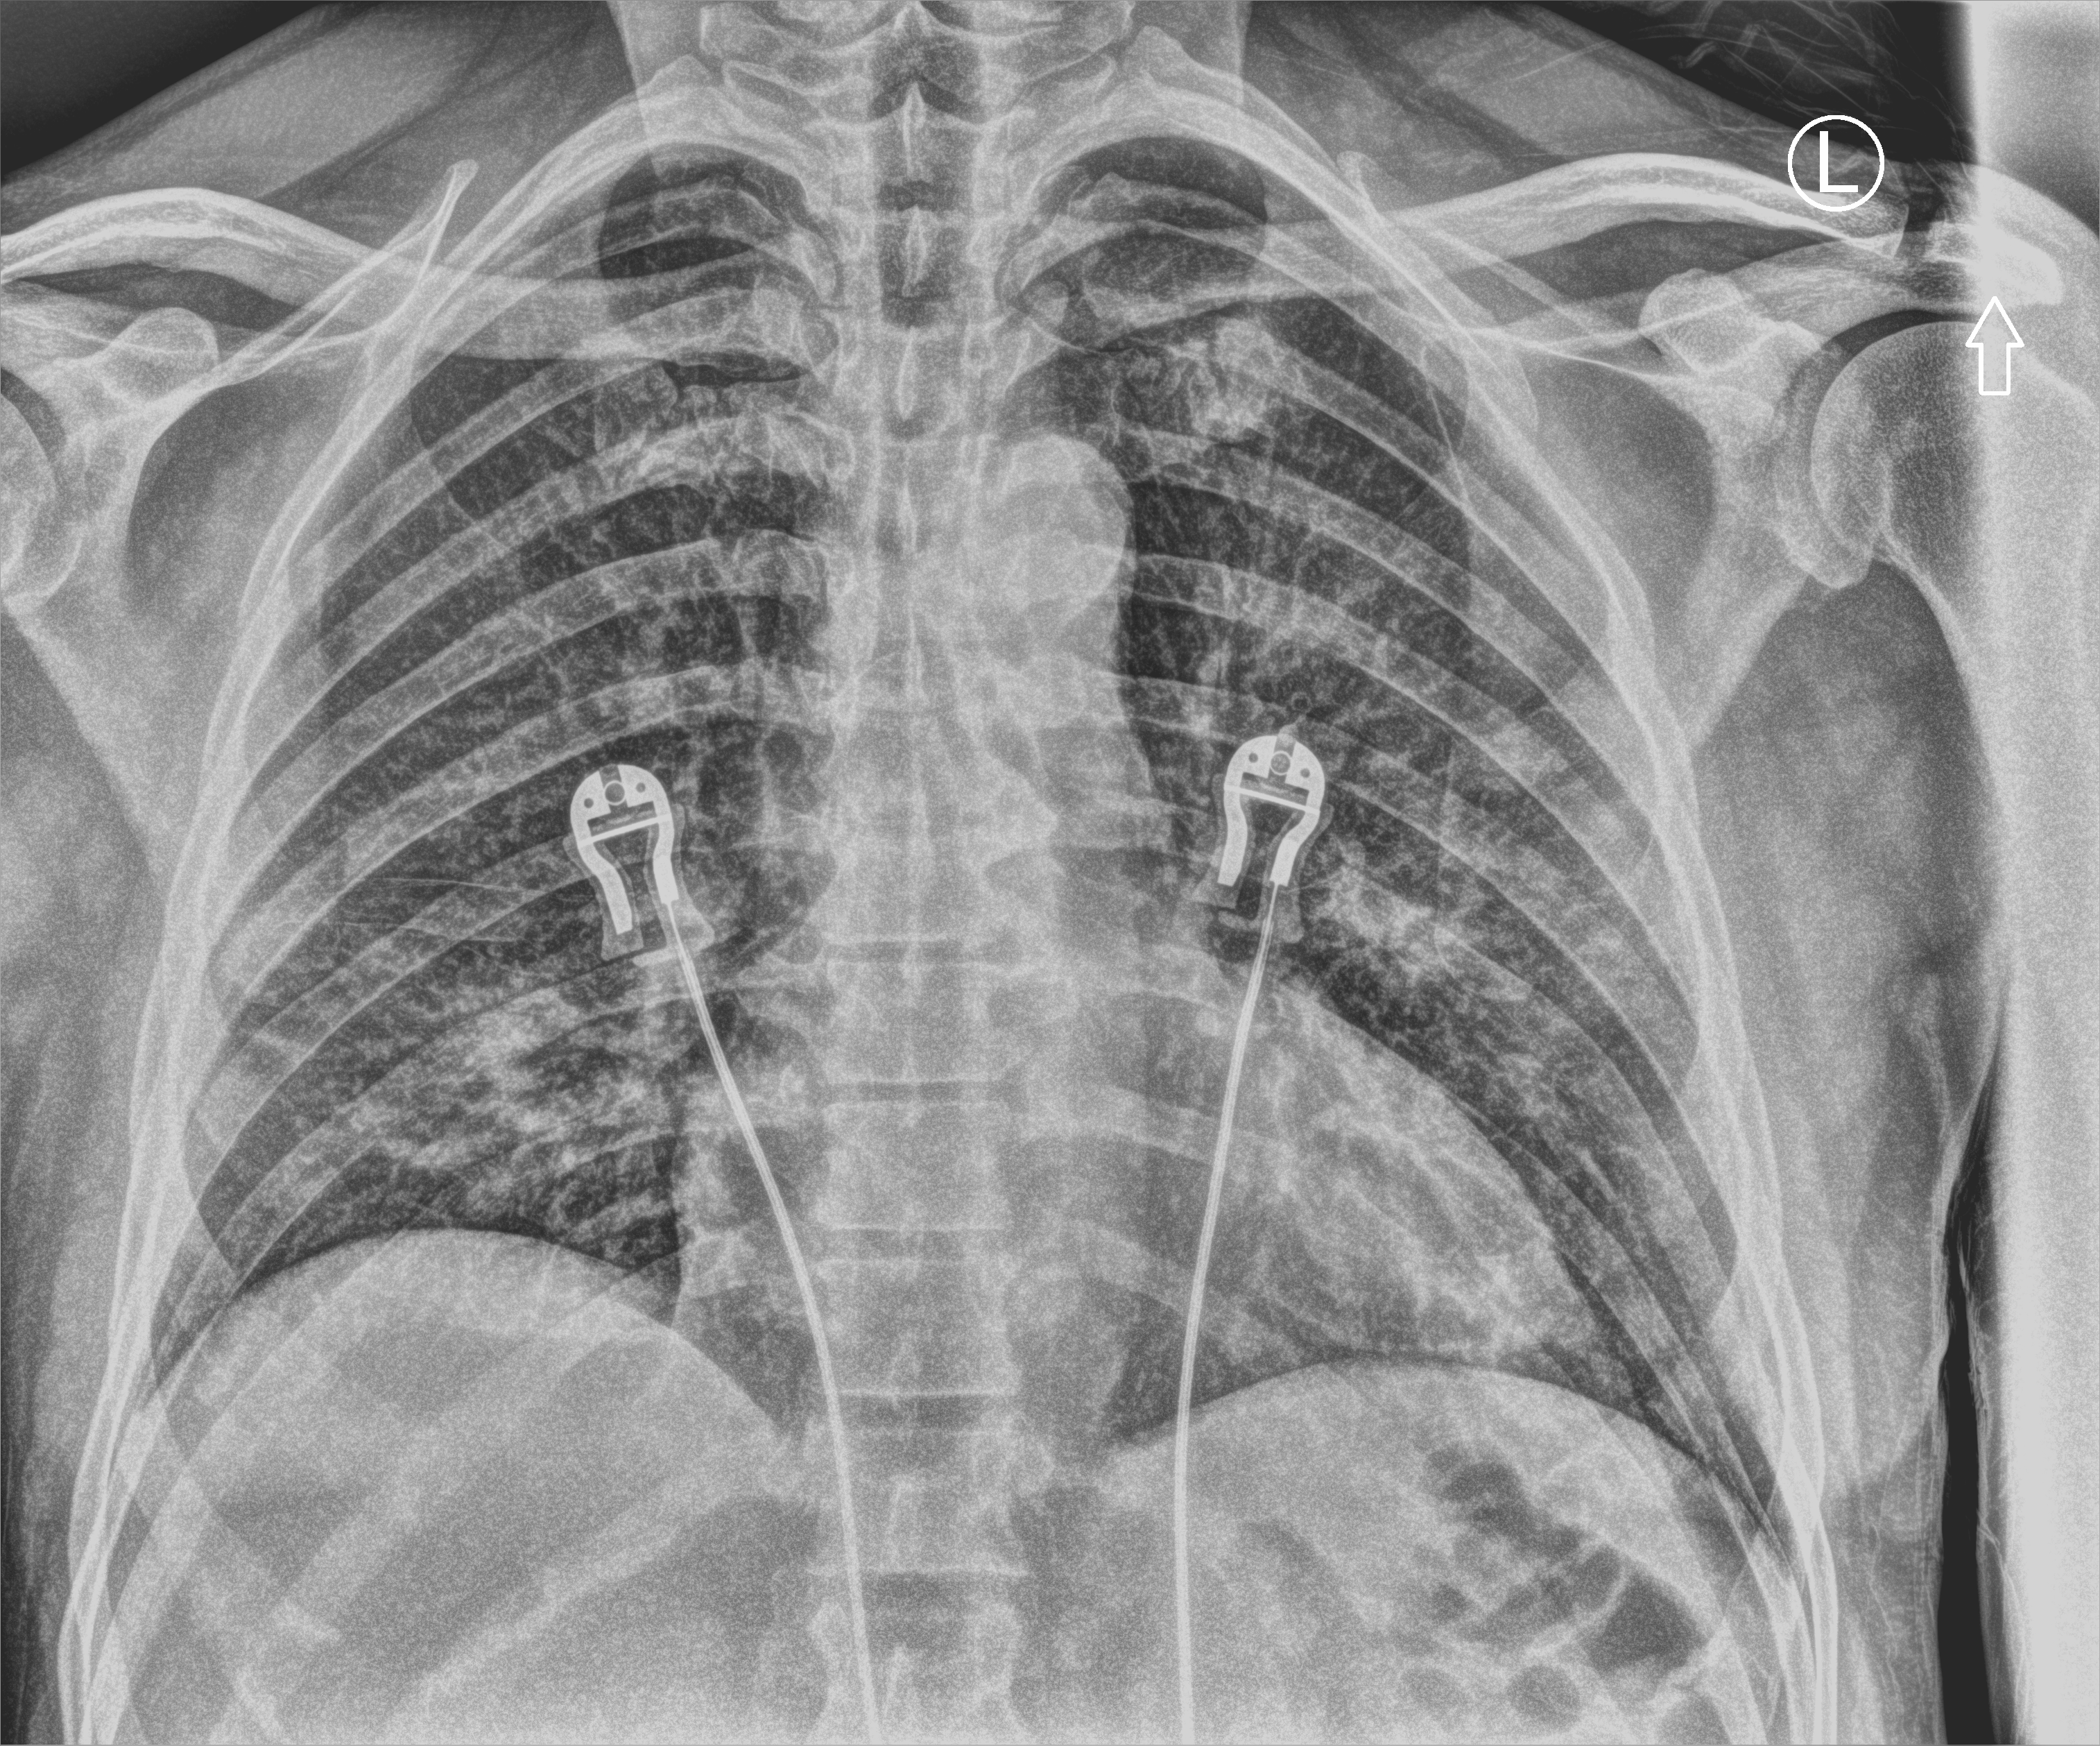
Portable chest radiograph; anteroposterior (AP) projection. Patient hospitalised with COVID-19; male, aged 18–59 years.
Hospital-stay facts (about this admission, not read from this image; timing relative to this image not recorded):
- mechanically ventilated during this hospital stay: no